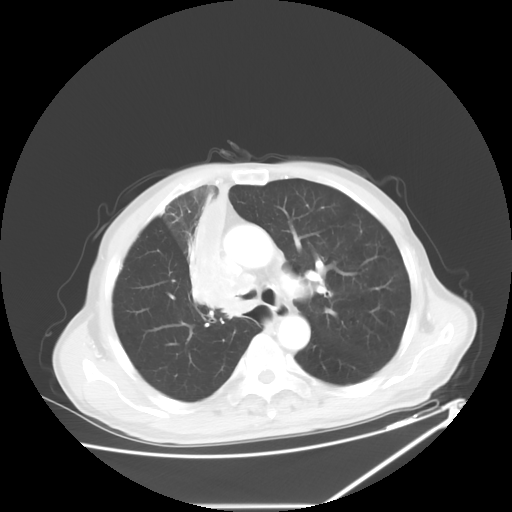
Chest CT, one axial slice. Slice 41 of 60 in the series (ordered by position). Lung window (W 1500 / L -600 HU). 5 mm slice thickness. 512 × 512 image matrix, field of view 410 × 410 mm. Male patient, age 73 years. From the clinical record (not read from this slice): clinical TNM (as recorded): T2a N1 M0.
Structures marked on this image (rectangle marked by the reading radiologist):
- lung tumour (recorded histology: squamous cell carcinoma): bounding box <184,175,263,321> (left, top, right, bottom; pixels)